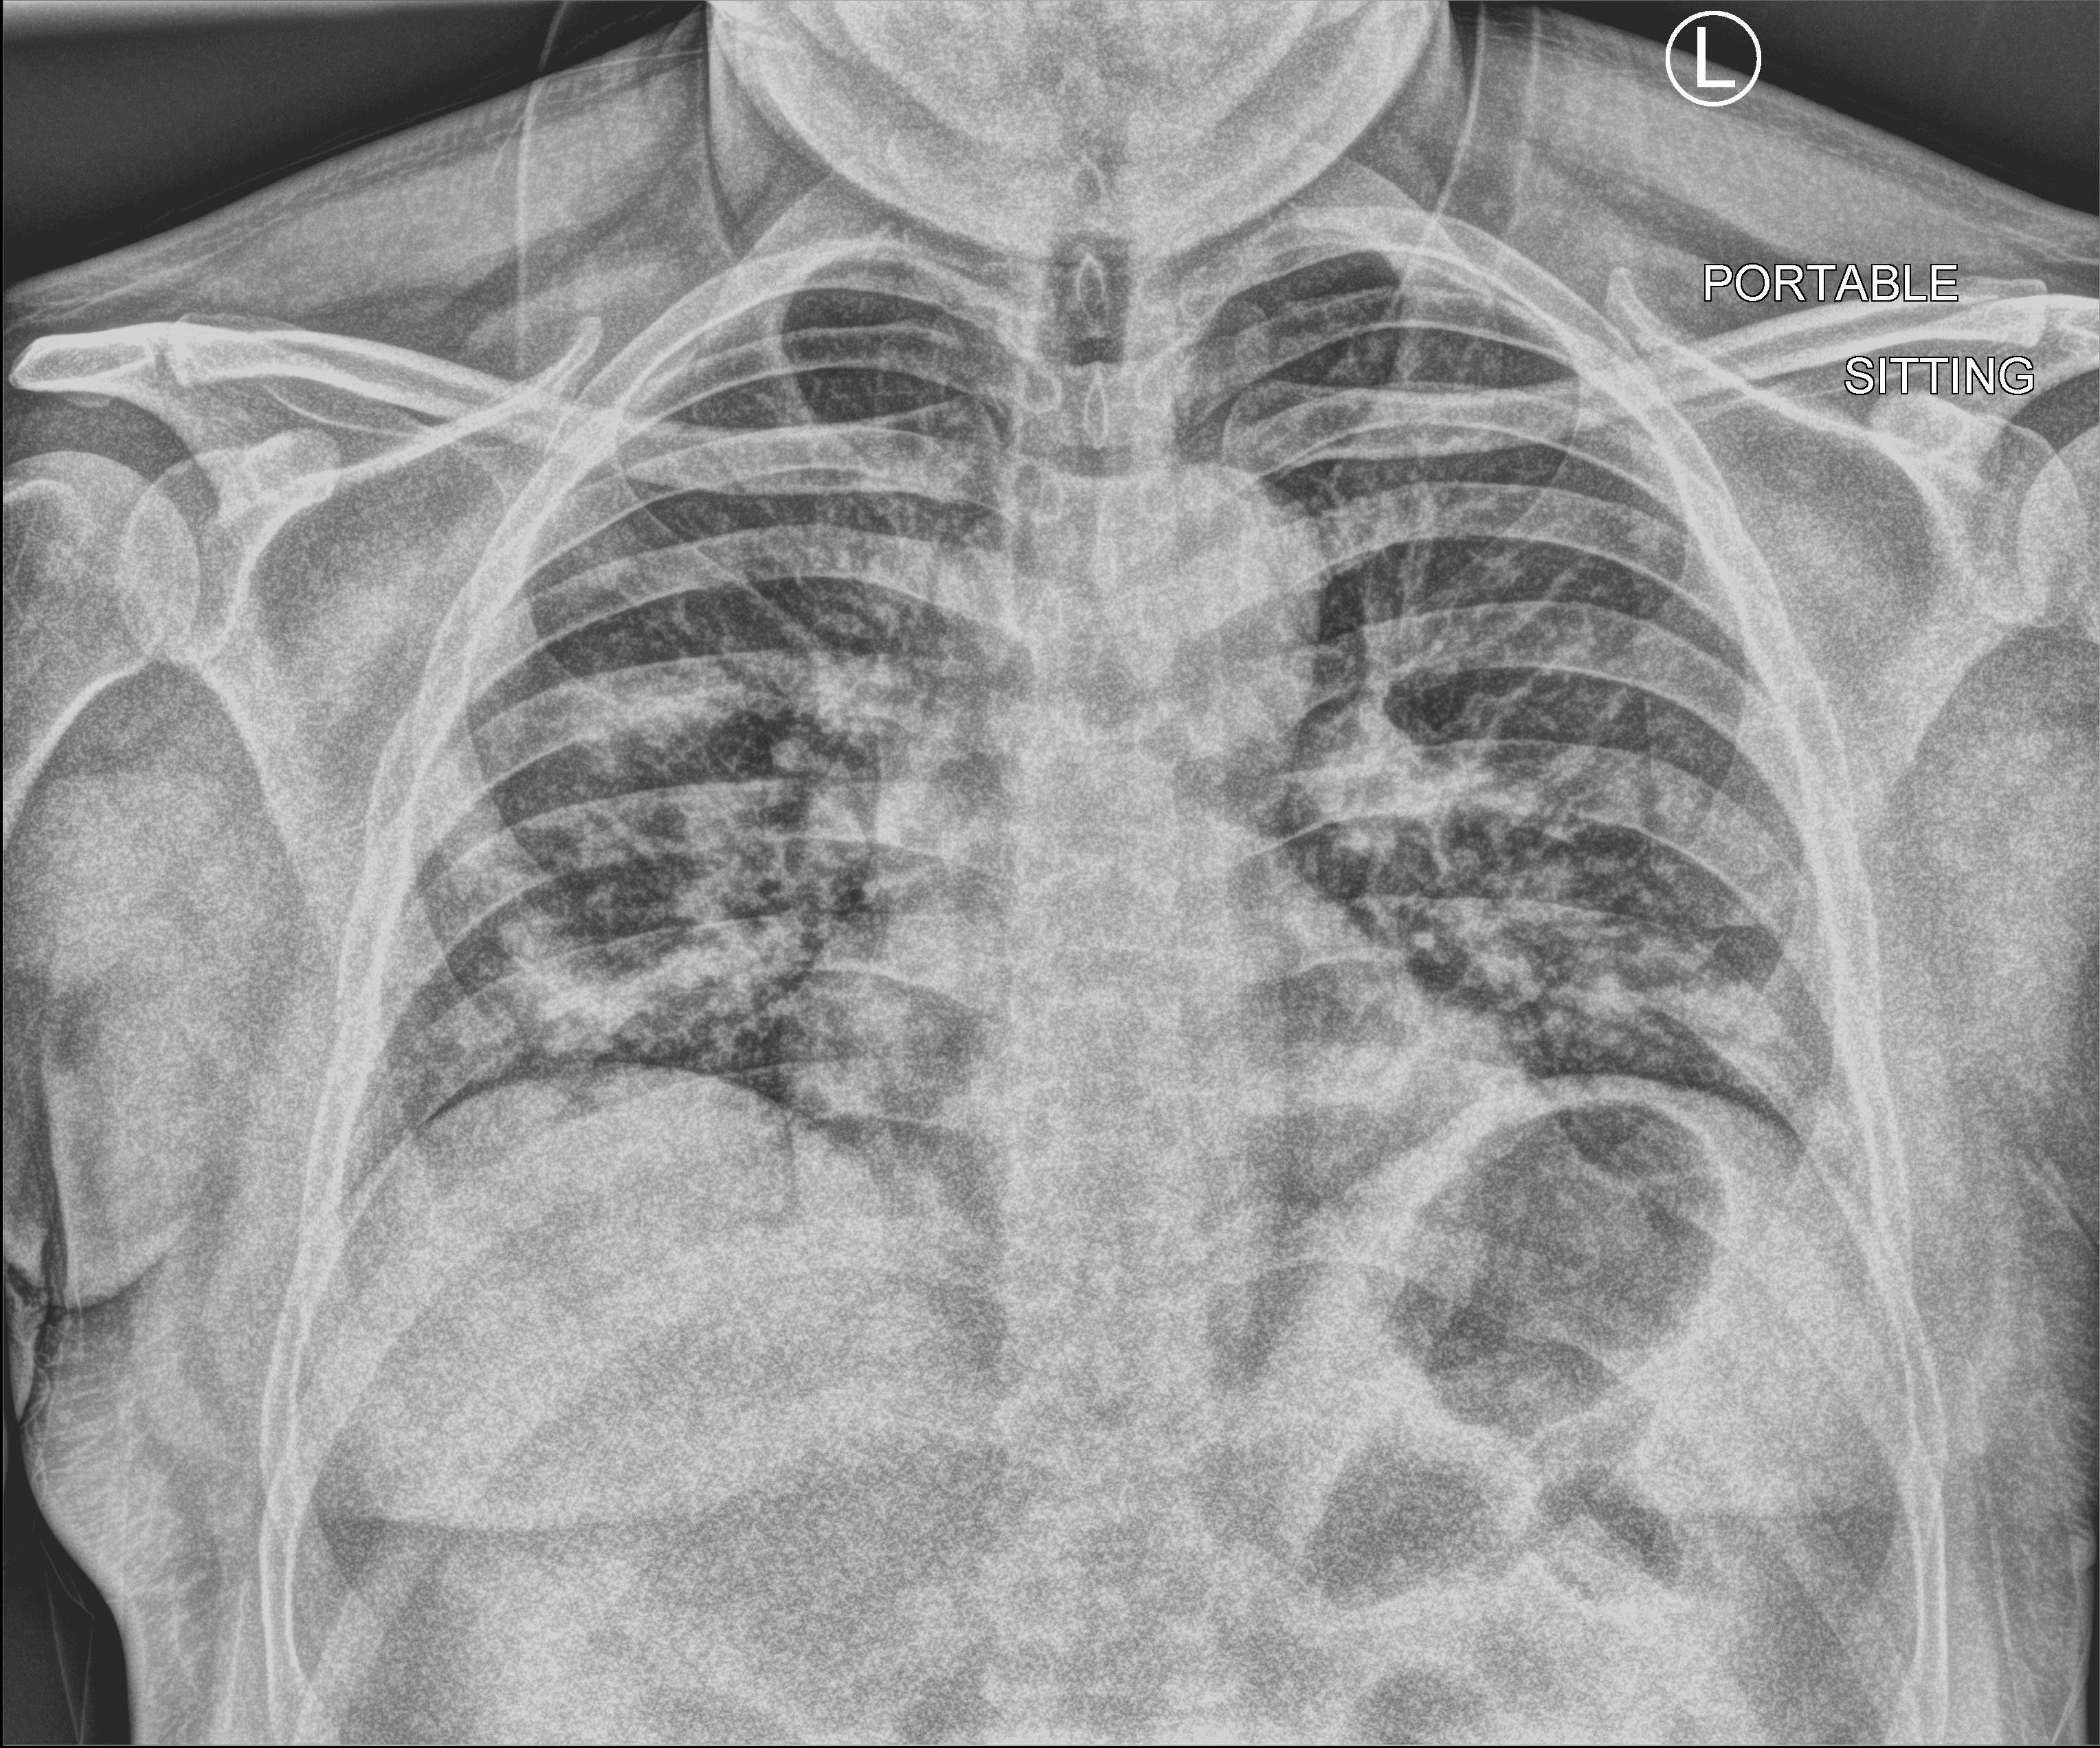
Chest X-ray (portable), anteroposterior (AP) projection. Male patient hospitalised with COVID-19, age 18–59 years.
Admission-level facts for this patient (not findings on this image; timing relative to this image not recorded):
- mechanically ventilated during this hospital stay: no